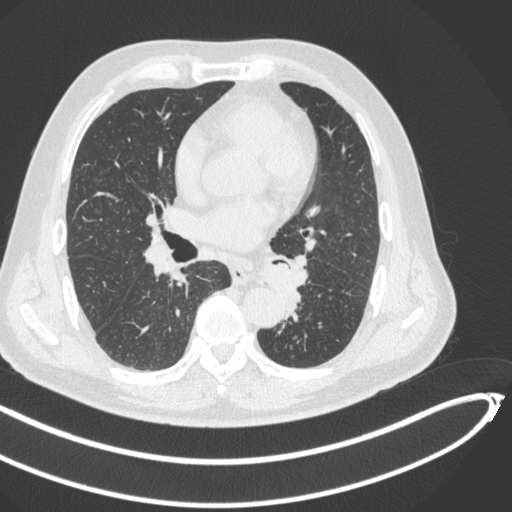
Chest CT, one axial slice. Position 243 of 466 along the scan axis. Reconstruction kernel B31f. Lung window (W 1500 / L -600 HU). 512 × 512 image matrix, field of view 400 × 400 mm. Patient: male, 64 years. Case-level facts recorded for this patient, not image findings: clinical TNM (as recorded): T1c N0 M0; histopathological grade: G2.
Annotated regions visible in this slice (rectangle marked by the reading radiologist):
- lung tumour (recorded histology: squamous cell carcinoma): bounding box <257,257,305,307> (left, top, right, bottom; pixels)